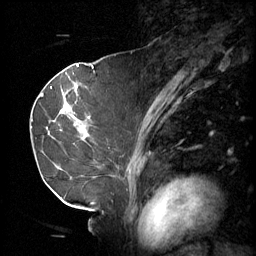
Breast MRI (dynamic contrast-enhanced), one sagittal slice. Slice 31 of 60 in the series (ordered by position). 3 images stored at this slice position (order not interpretable as contrast timing). 1.5 T. TE 4.2 ms, TR 11 ms. 2 mm slice thickness. 256 × 256 image matrix, field of view 220 × 220 mm. Female patient, age 69 years.
Outlined on this slice (semi-automatic segmentation, software-assisted and operator-edited):
- analysis volume of interest (the breast-tissue region the enhancement analysis was run in; not a lesion): bounding box [x1, y1, x2, y2] px = [36, 88, 97, 189]
- tumour enhancement mask (voxels above the 70 % enhancement threshold inside the analysis volume of interest): [62, 88, 86, 139]